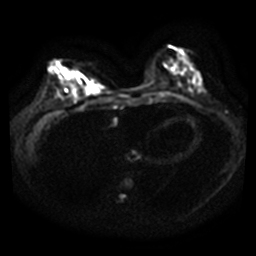
Breast MRI, one axial slice; slice 13 of 40 in the series (ordered by position); diffusion-weighted series; image 2 of 4 stored at this slice position (different b-values; order by instance number); 3 T; 5 mm slice thickness; 256 × 256 image matrix, field of view 340 × 340 mm. Female patient.
Annotated regions visible in this slice (expert manual segmentation):
- tumour on diffusion-weighted imaging: bounding box (x1, y1, x2, y2) in pixels: (74, 70, 97, 92)